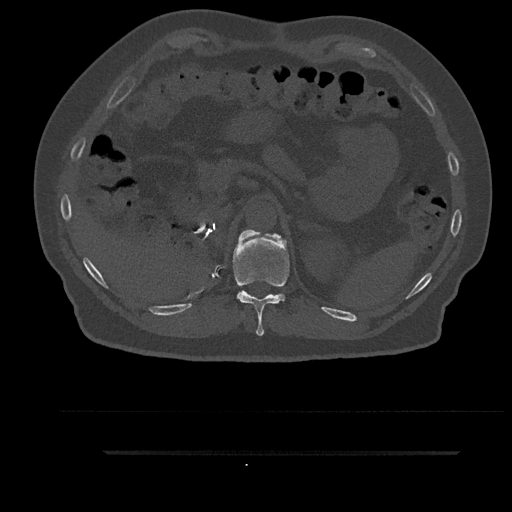
CT including the spine, one axial slice; slice 294 of 797 in the series (ordered by position); reconstruction kernel Br40s/3; 120 kVp; bone window (W 1800 / L 400 HU); 0.5 mm slice thickness; 512 × 512 image matrix, field of view 432 × 432 mm. Male patient, age 63 years. From the clinical record (not read from this slice): primary cancer: renal; vertebrae with lytic lesions (as recorded): T8.
Structures marked on this image (semi-automatic segmentation, software-assisted and operator-edited):
- T11 vertebra: box from (x=233, y=230) to (x=289, y=336) px